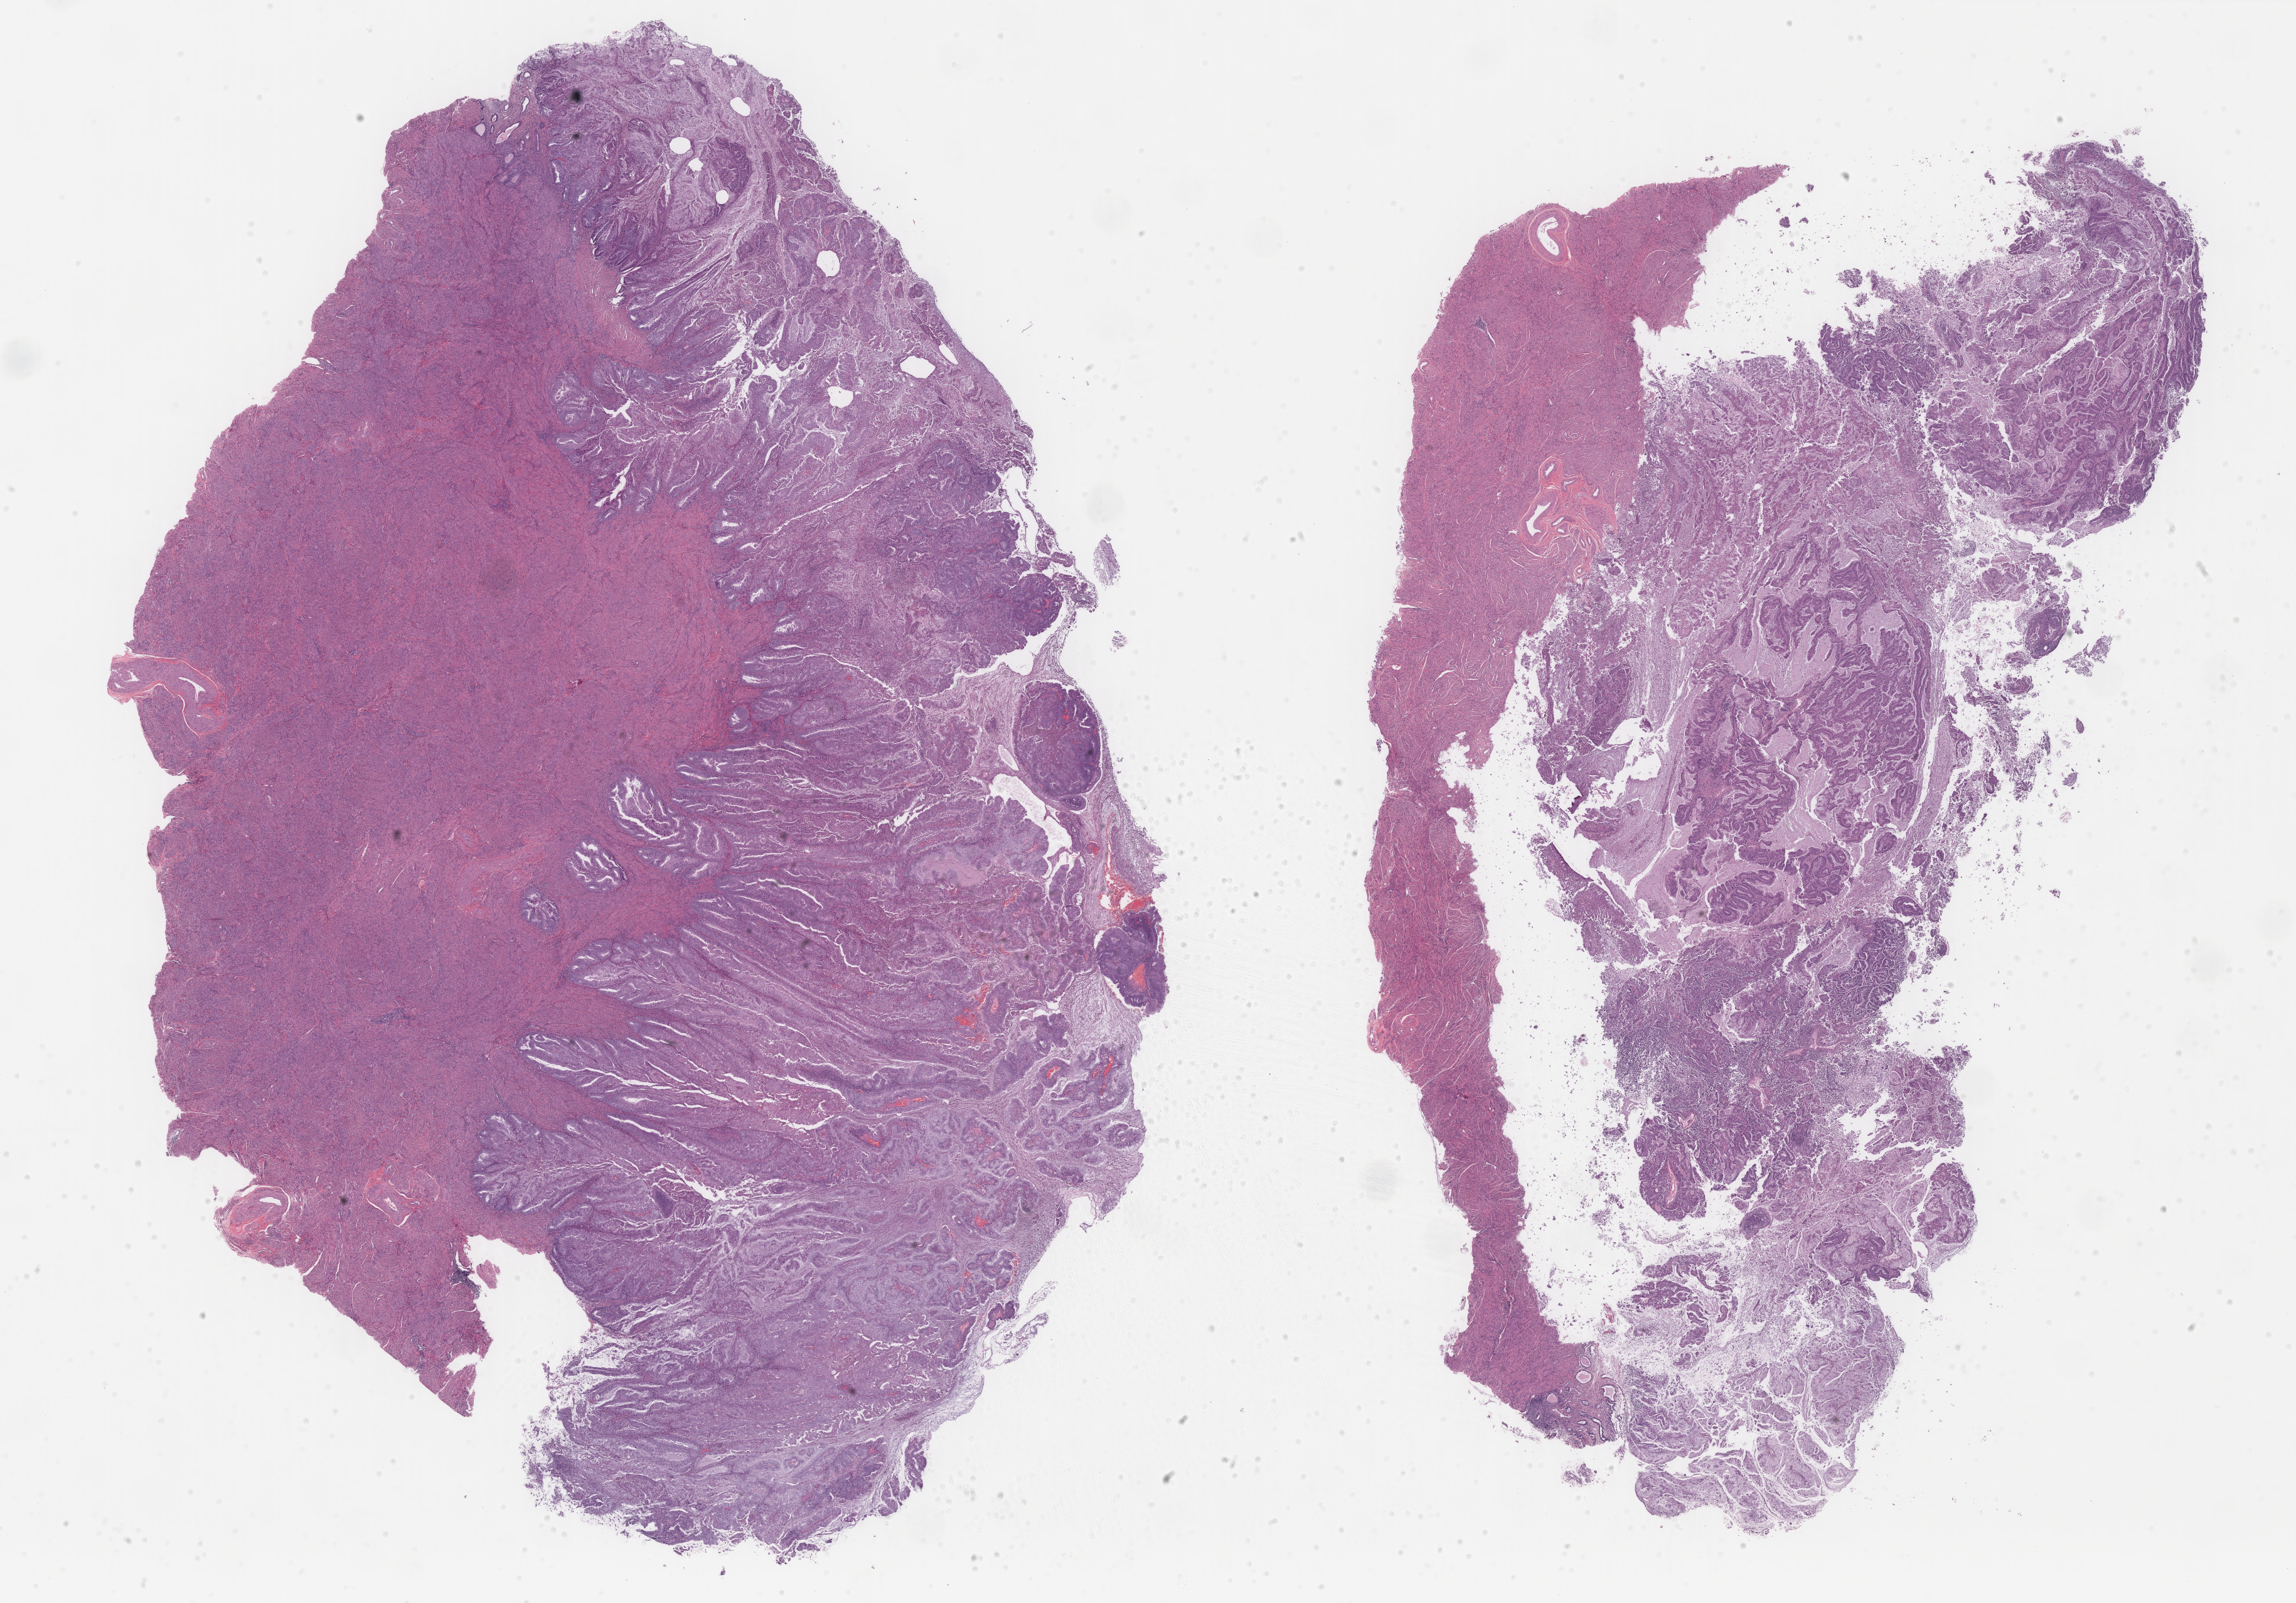
Hematoxylin and eosin (H&E) stained whole-slide image — shown as a low-resolution overview of the whole scanned area (about 29.0 x 20.3 mm). Formalin-fixed paraffin-embedded (FFPE) diagnostic section. Sample: primary tumour, uterus. Female patient; age at initial diagnosis 53 years. Histologic grade: G1 (well differentiated).
* diagnosis: Endometrioid adenocarcinoma, NOS (endometrium)
* FIGO stage: IA